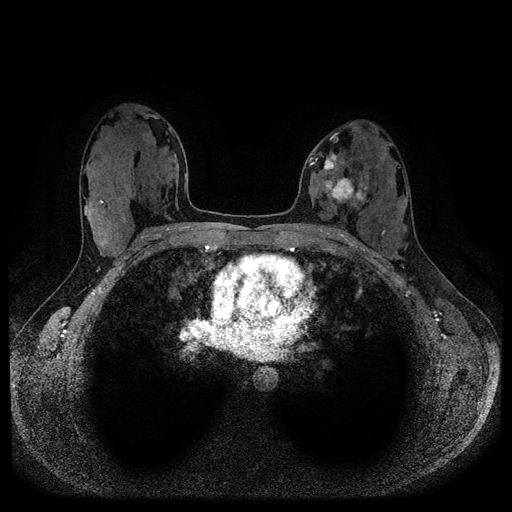
Breast MRI (dynamic contrast-enhanced, multi-phase), one axial slice; slice 58 of 116 in the series (ordered by position); dynamic contrast-enhanced series, time point 2 of 5 at this slice position (early post-contrast); 1.5 T; TE 2.6 ms, TR 5.3 ms; 2 mm slice thickness; 512 × 512 image matrix. Patient: female, 33 years.
Structures marked on this image (semi-automatically segmented with operator editing):
- breast lesion (labelled 'tumour' in the annotation; benign lesions carry a separate 'benign' label): box from (x=320, y=152) to (x=365, y=205) px